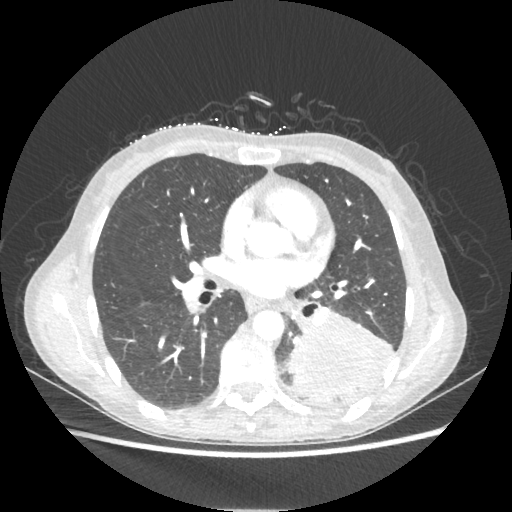
Chest CT, one axial slice; position 111 of 221 along the scan axis; reconstruction kernel STANDARD; lung window (W 1500 / L -600 HU); 1.25 mm slice thickness; 512 × 512 image matrix, field of view 360 × 360 mm. Patient: female, 53 years. Case-level facts recorded for this patient, not image findings: clinical TNM (as recorded): T3 N0 M0.
Outlined on this slice (bounding box drawn by a radiologist):
- lung tumour (recorded histology: adenocarcinoma): box from (x=286, y=313) to (x=394, y=400) px